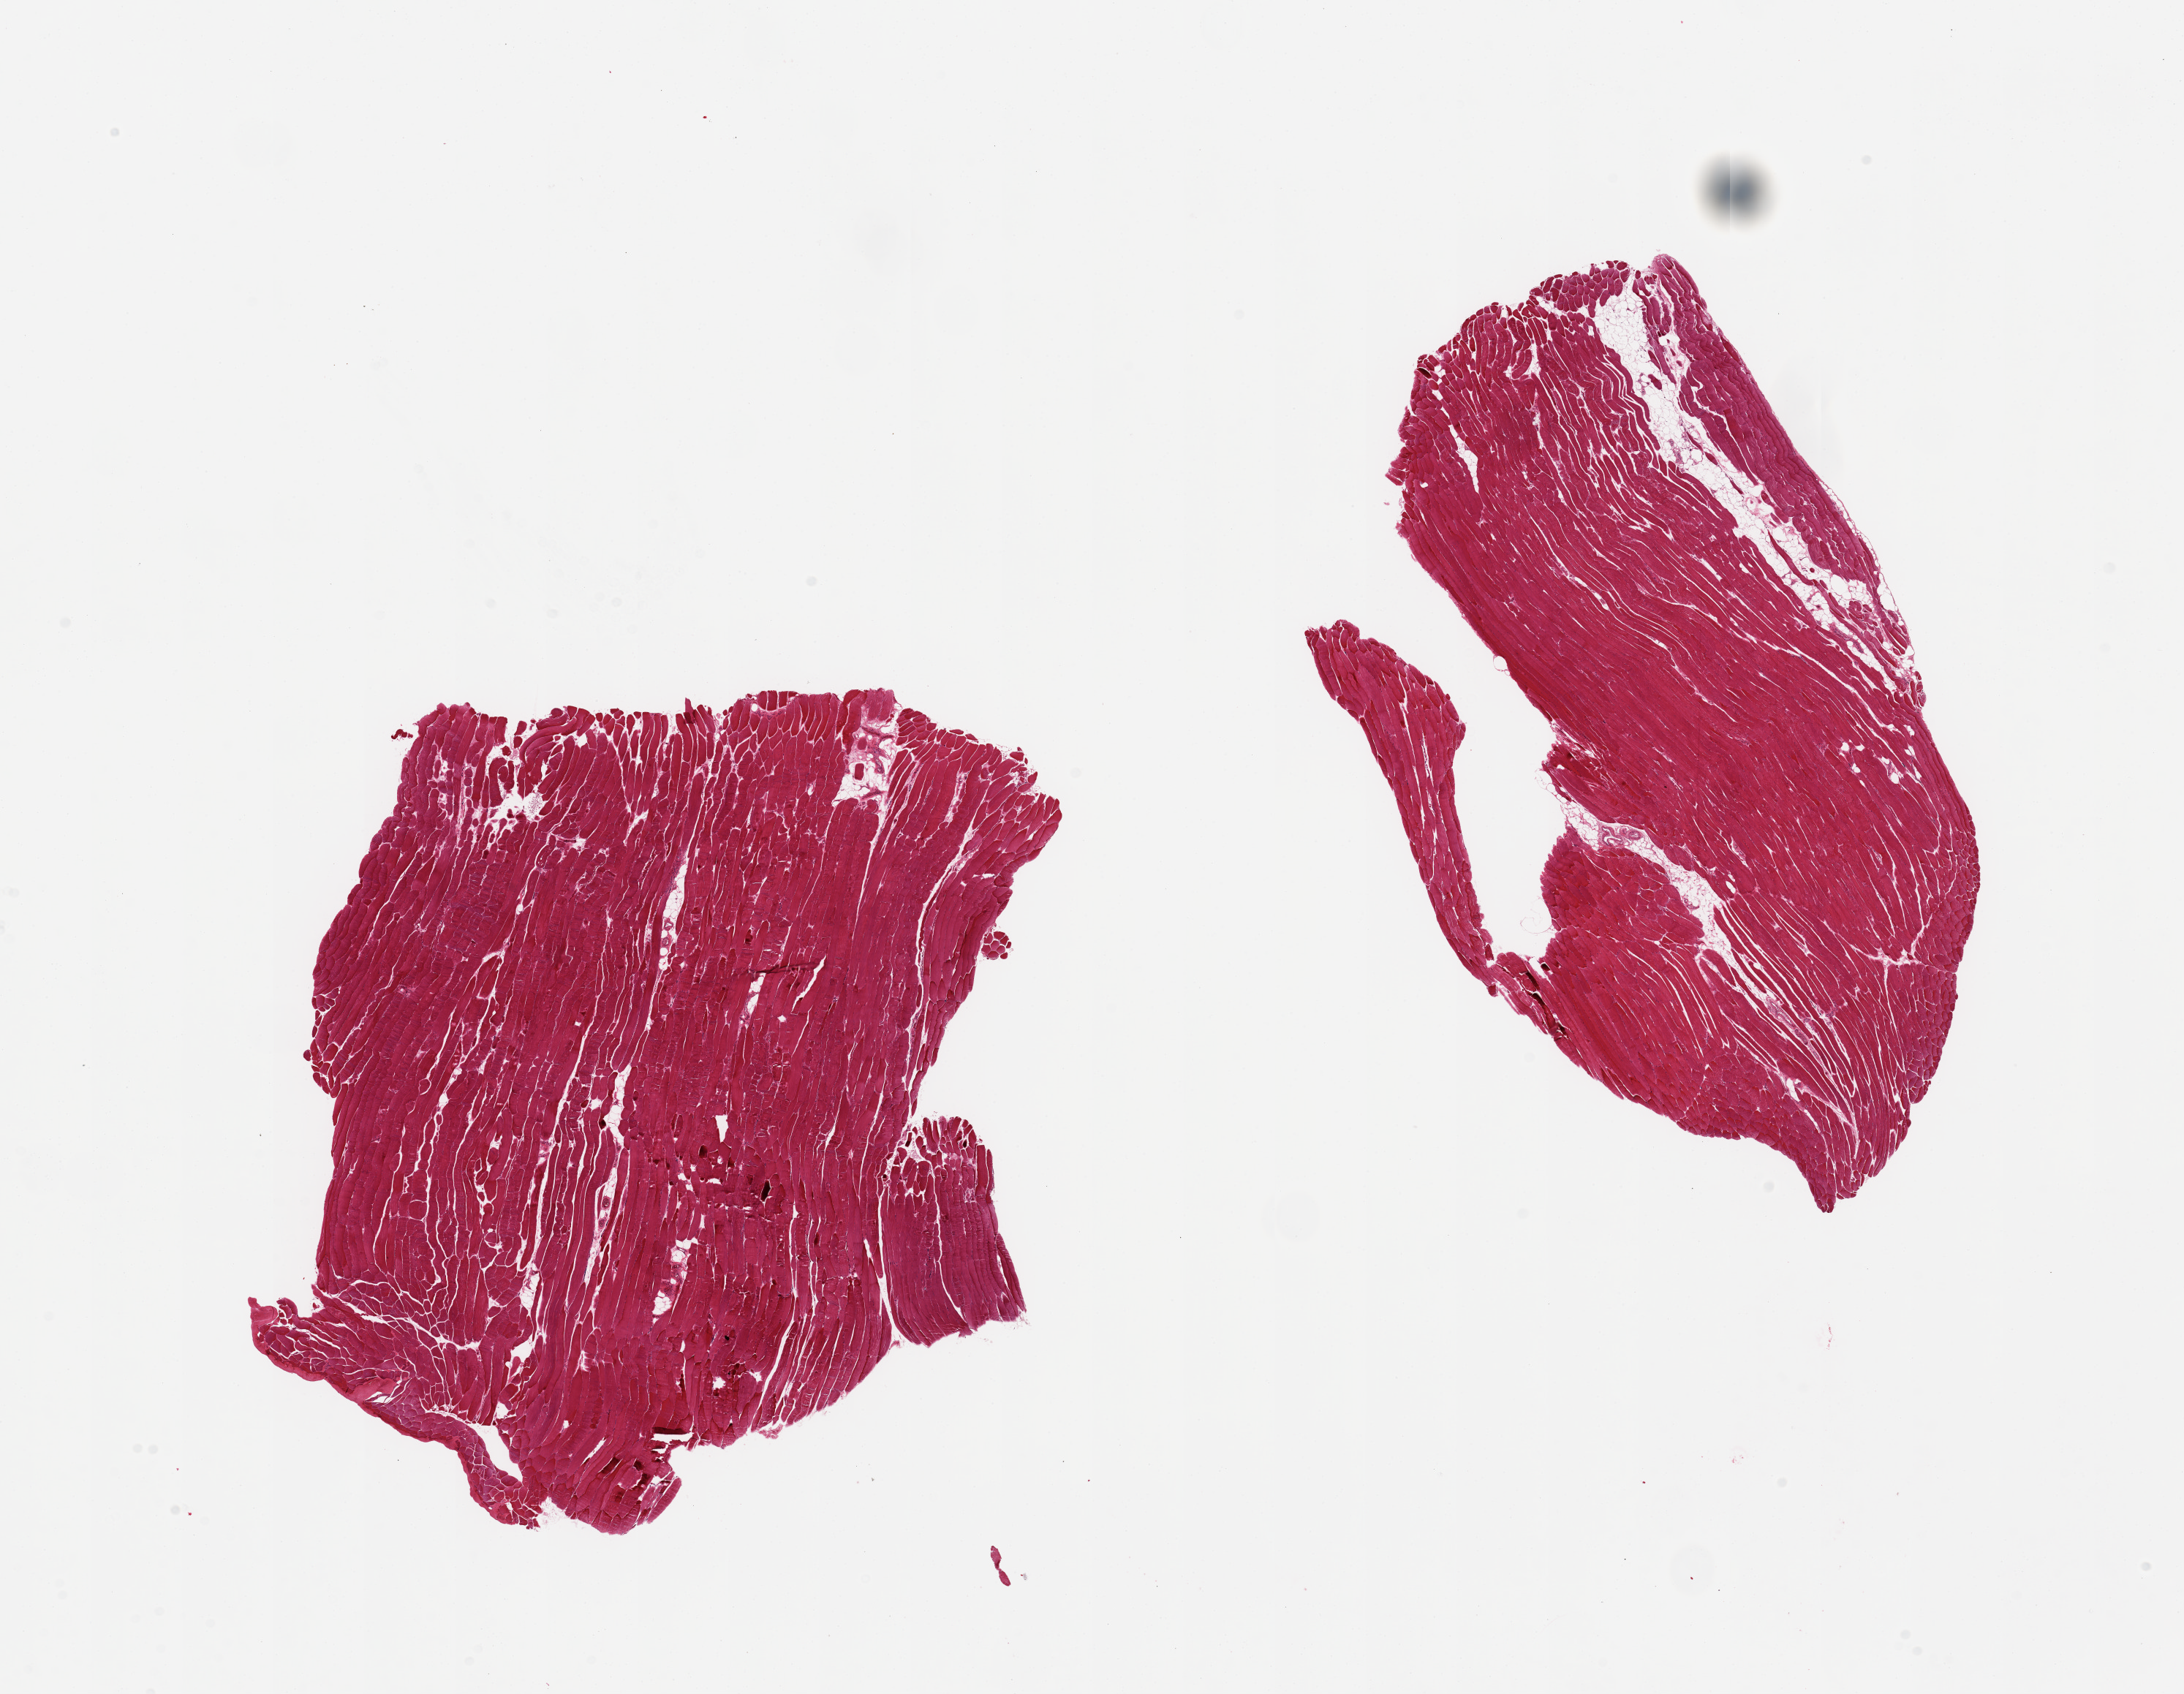
Whole-slide image, hematoxylin and eosin (H&E) stain, a low-resolution overview of the entire scanned area, about 23.6 x 18.3 mm (from a 20x scan); PAXgene-fixed, paraffin-embedded tissue; section of skeletal muscle (target tissue); tissue donor sample. Male donor.
Review note (as recorded): 2 pieces; less than 10% of internal fat.